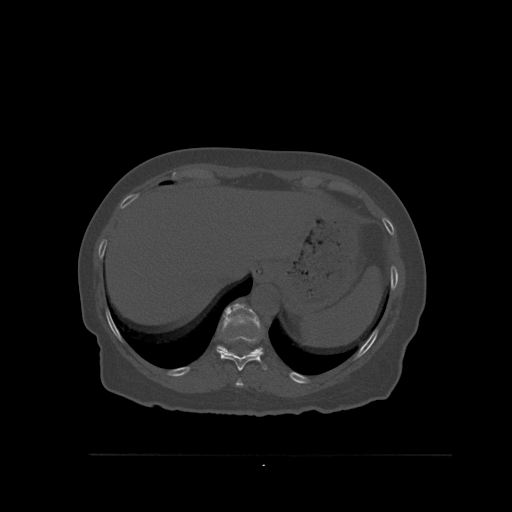
CT including the spine, one axial slice; slice 316 of 527 in the series (ordered by position); bone window (W 1800 / L 400 HU); 1.5 mm slice thickness; 512 × 512 image matrix. Patient: female, 73 years. From the clinical record (not read from this slice): primary cancer: breast.
Annotated regions visible in this slice (semi-automatically segmented with operator editing):
- T10 vertebra: box from (x=216, y=336) to (x=267, y=371) px
- T11 vertebra: (x=217, y=303)–(x=263, y=356)
- T9 vertebra: (x=235, y=379)–(x=244, y=387)